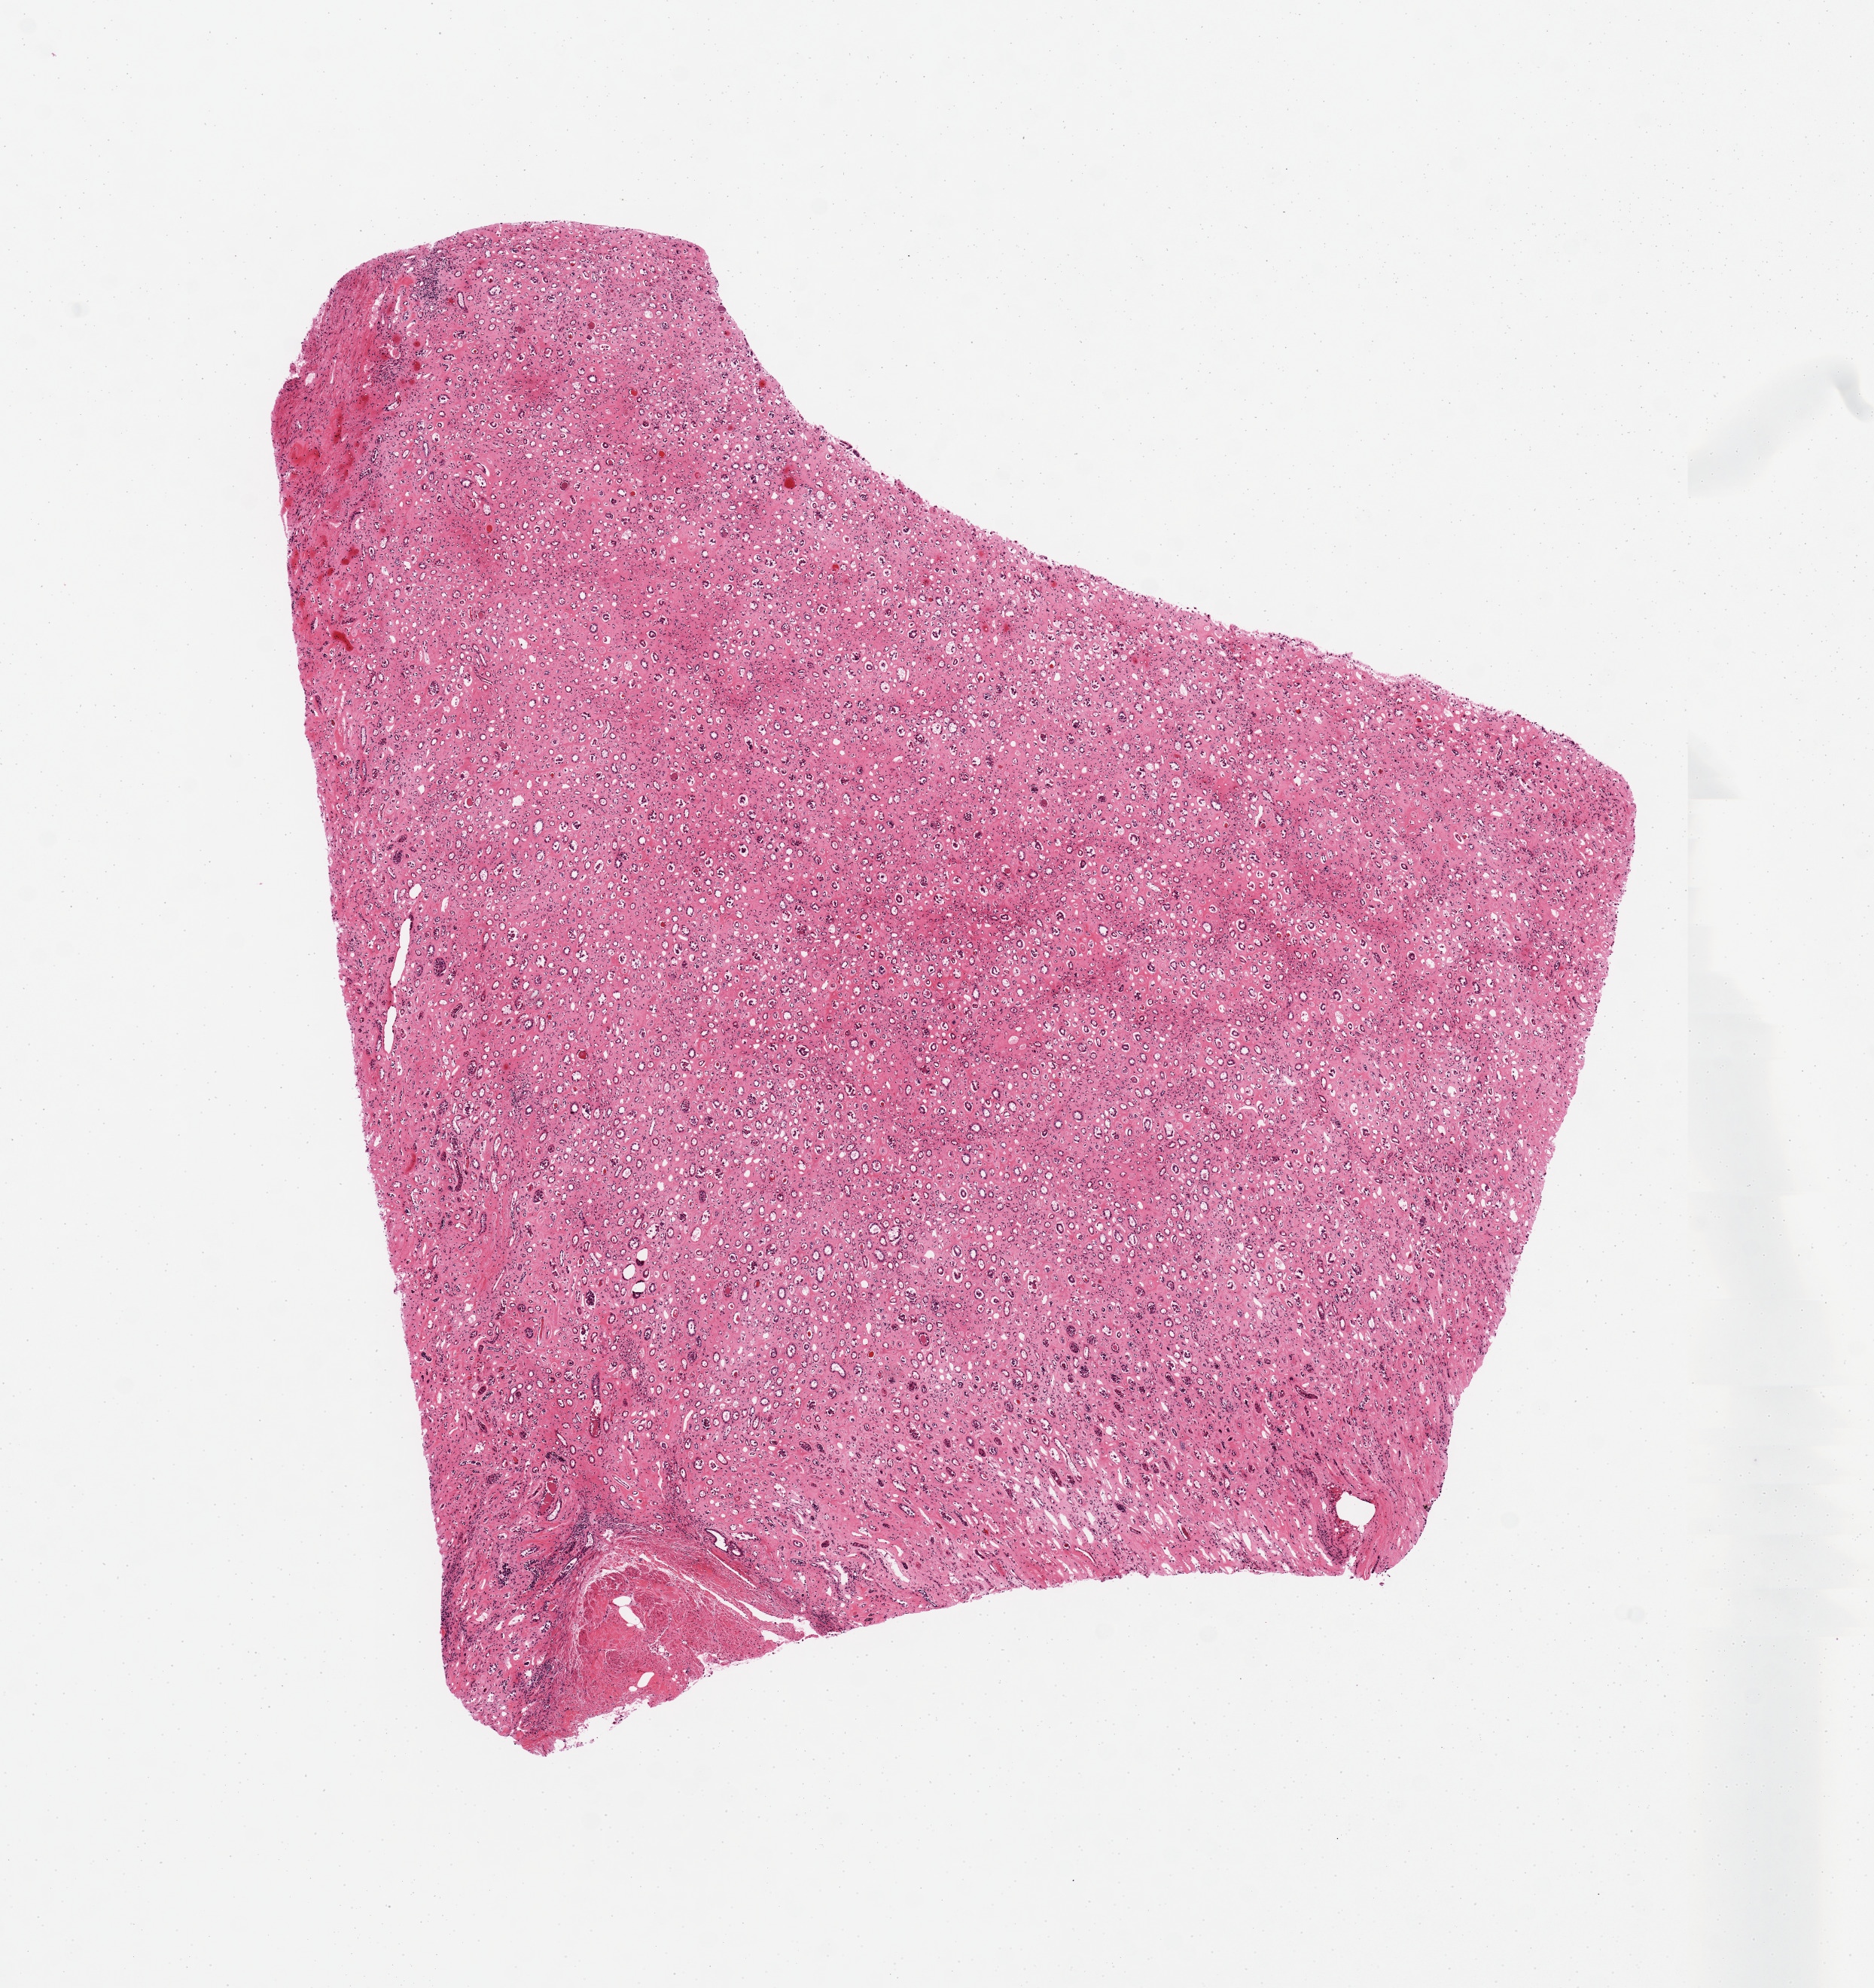
Digitized haematoxylin and eosin-stained section, a low-resolution overview of the entire scanned area, about 9.8 x 10.4 mm; PAXgene-fixed paraffin-embedded (PFPE) section; sampled site (target tissue): renal medulla; donor tissue sample. Donor: male.
Review note (as recorded): Moderate fibrosis.